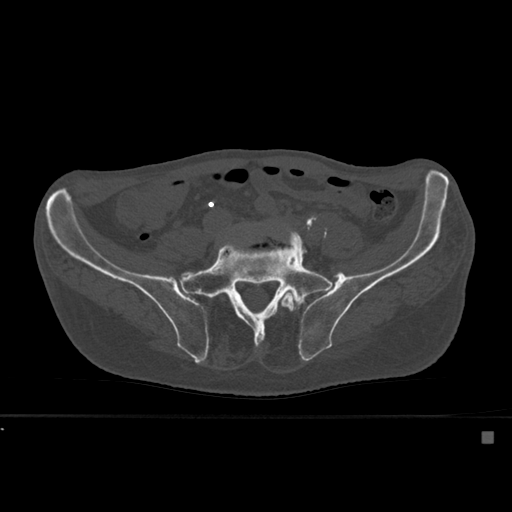
CT including the spine, one axial slice. Position 163 of 527 along the scan axis. Bone window (W 1800 / L 400 HU). 1.5 mm slice thickness. 512 × 512 image matrix, field of view 373 × 373 mm. Male patient, age 78 years. From the clinical record (not read from this slice): primary cancer: prostate.
Structures marked on this image (semi-automatic segmentation, software-assisted and operator-edited):
- L5 vertebra: bounding box <222,234,296,312> (left, top, right, bottom; pixels)